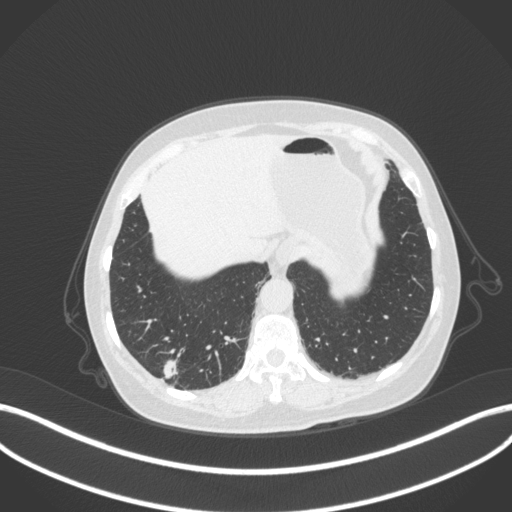
Chest CT, one axial slice; reconstruction kernel B31f; 120 kVp; lung window (W 1500 / L -600 HU); 1 mm slice thickness; 512 × 512 image matrix, field of view 400 × 400 mm. Female patient, age 69 years. From the clinical record (not read from this slice): clinical TNM (as recorded): T1b N0 M0; histopathological grade: G2-3.
Structures marked on this image (bounding box drawn by a radiologist):
- lung tumour (recorded histology: adenocarcinoma): bounding box (x1, y1, x2, y2) in pixels: (160, 355, 181, 382)